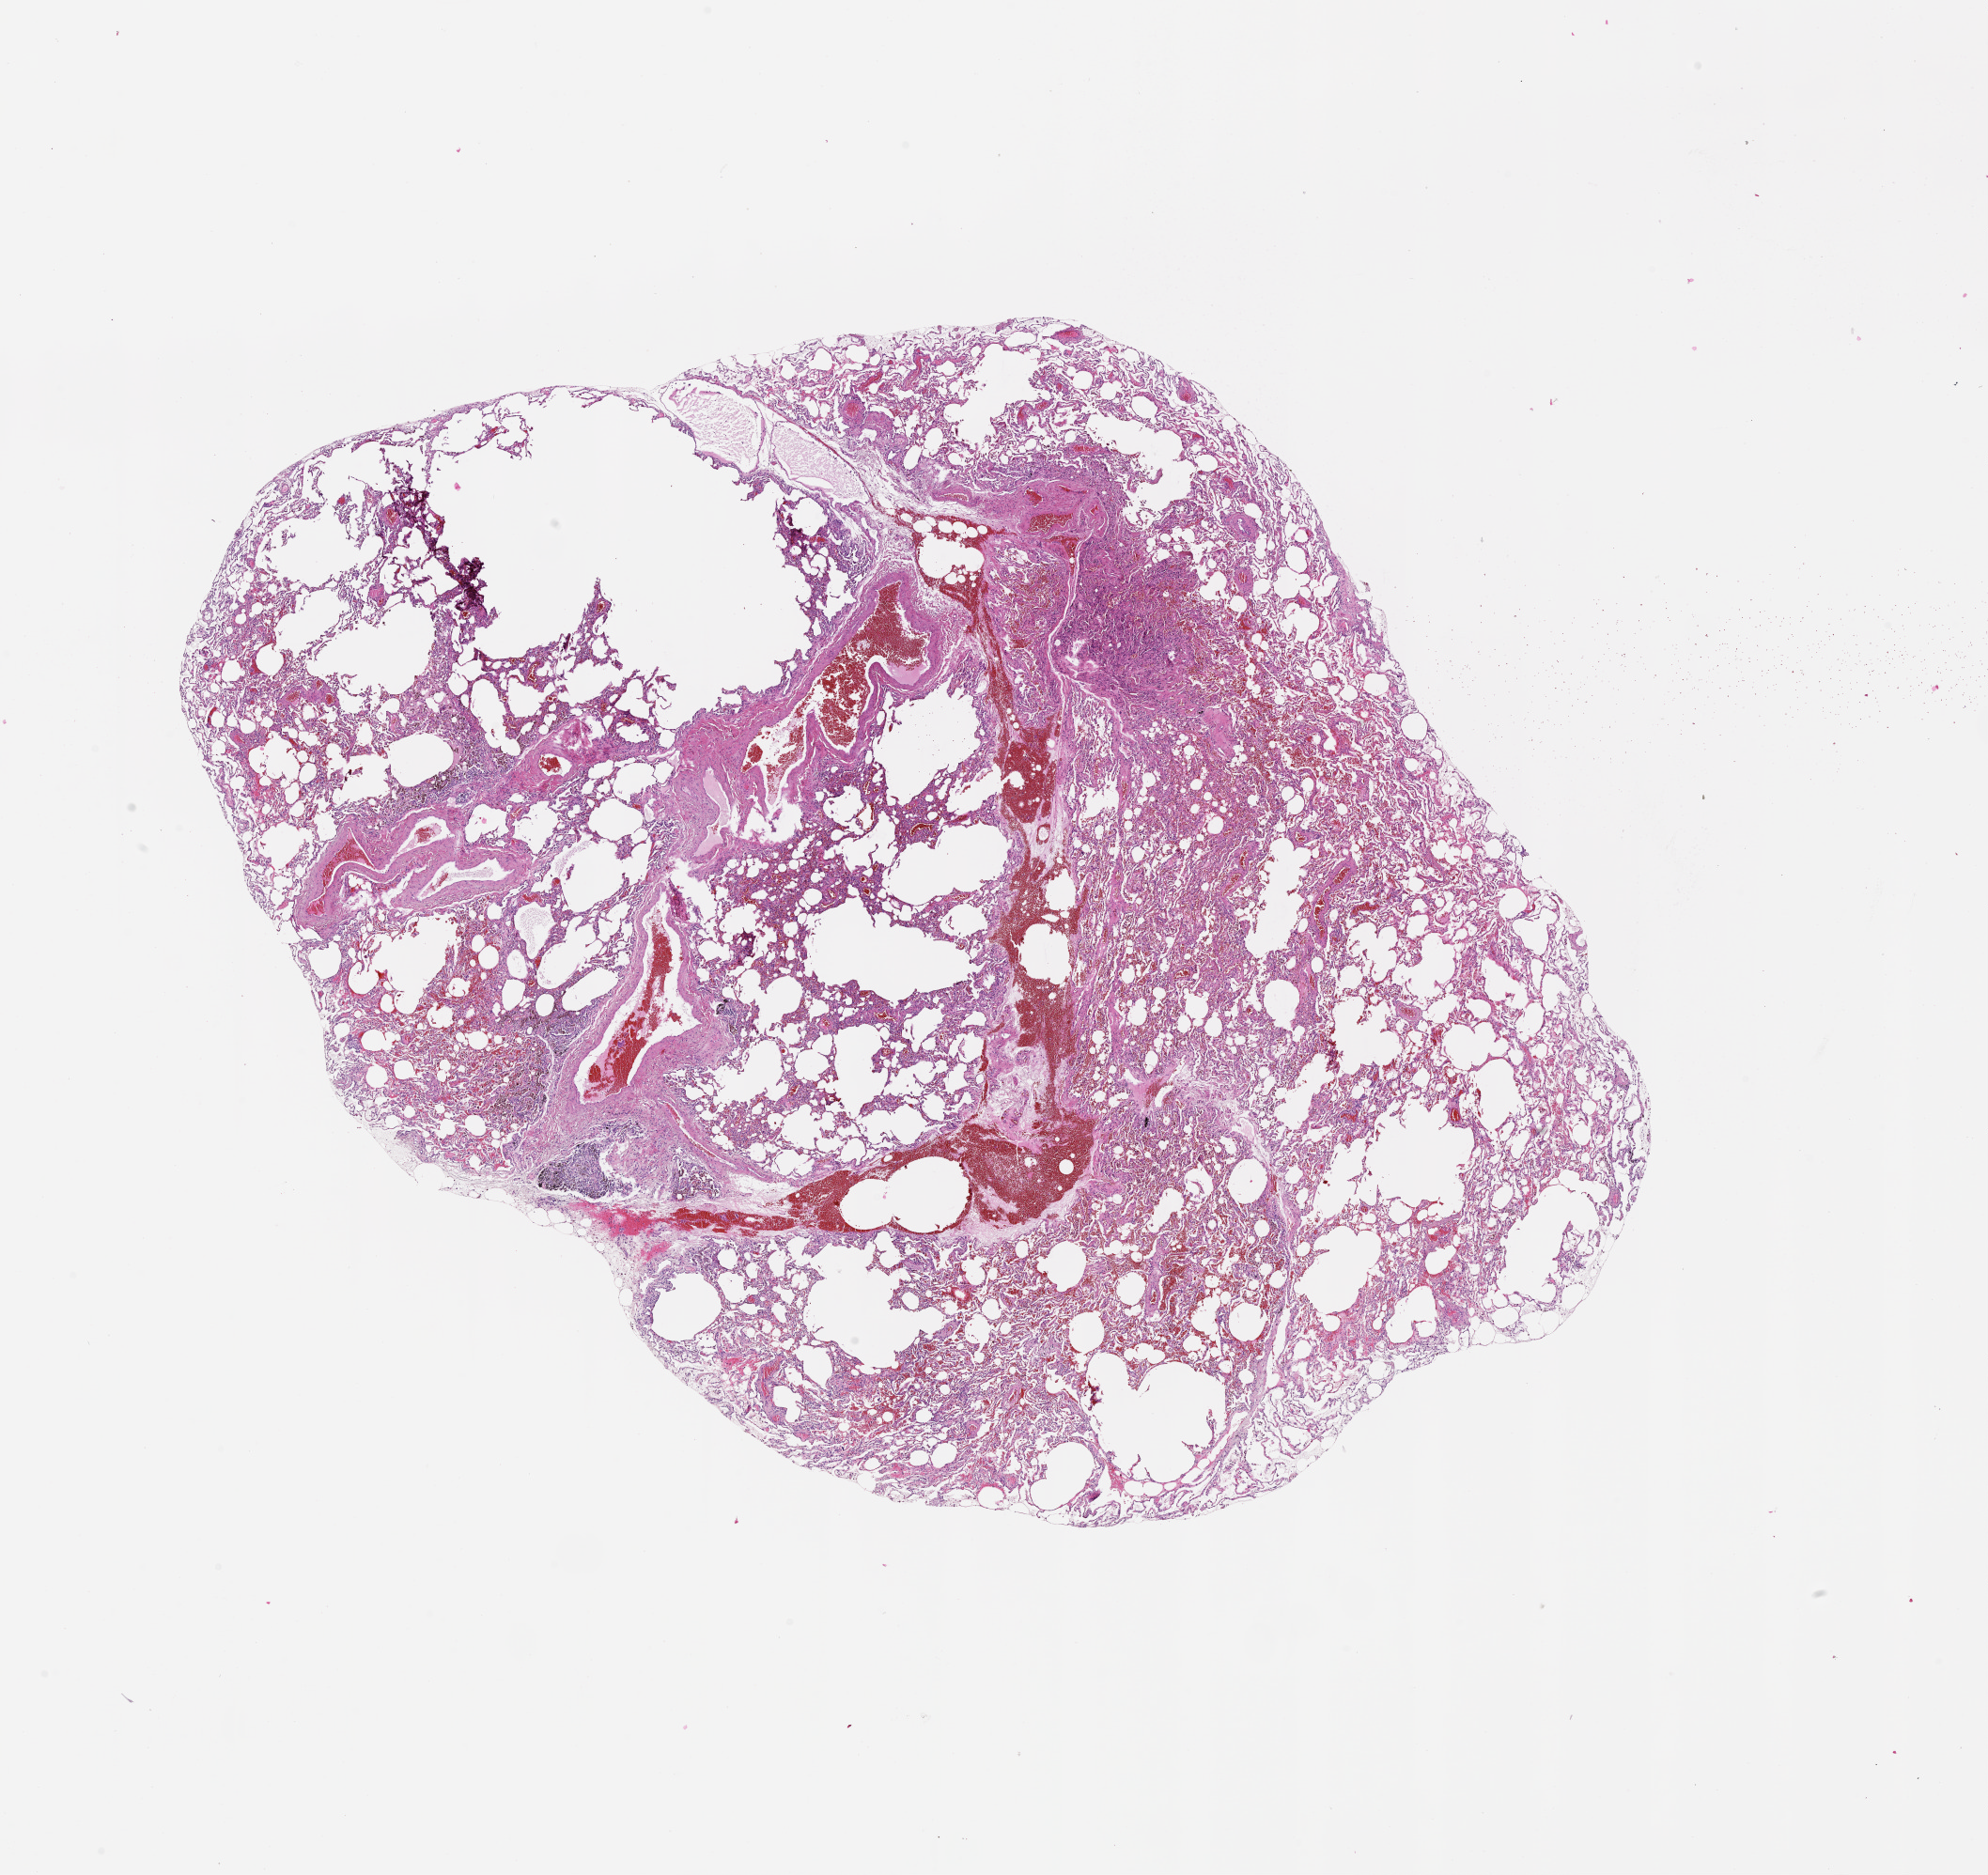
H&E whole-slide image — shown as a low-resolution overview of the whole scanned area (about 17.0 x 16.1 mm); normal (non-tumour) tissue sample, lung. Male, 60 y/o.
This section: normal (non-tumour) tissue from the same patient. Patient diagnosis (cohort enrolment): squamous cell carcinoma (lung).